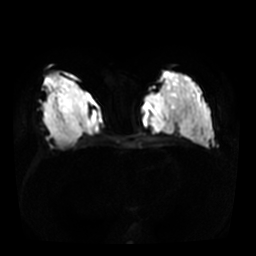
Breast MRI, one axial slice. Slice 16 of 36 in the series (ordered by position). Diffusion-weighted series; image 2 of 4 stored at this slice position (different b-values; order by instance number). 3 T. 5 mm slice thickness. 256 × 256 image matrix, field of view 340 × 340 mm. Female patient.
Structures marked on this image (outlined manually by an expert reader):
- tumour on diffusion-weighted imaging: bounding box [x1, y1, x2, y2] px = [165, 111, 180, 134]